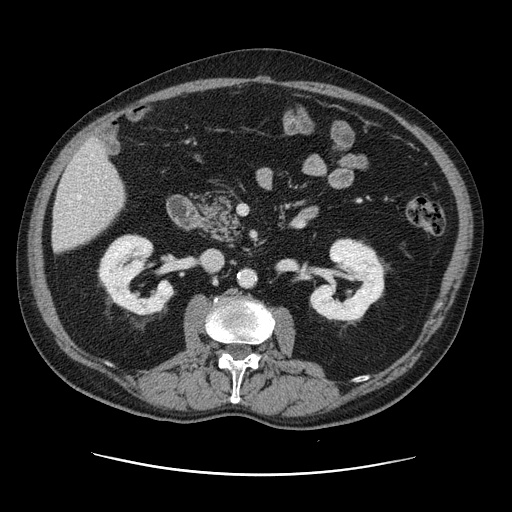
Contrast-enhanced abdominal CT, one axial slice; slice 46 of 141 in the series (ordered by position); 120 kVp; intravenous contrast given; soft-tissue window (W 400 / L 40 HU); 512 × 512 image matrix, field of view 395 × 395 mm. Male patient, age 72 years. Case-level facts recorded for this patient, not image findings: diagnosis: colorectal cancer liver metastases, imaged before liver resection; multiple liver metastases: yes; largest metastasis: 5.4 cm; chemotherapy before resection: yes.
Structures marked on this image (manually delineated by an expert):
- hepatic veins: bounding box (x1, y1, x2, y2) in pixels: (69, 195, 93, 203)
- liver: (54, 140, 126, 252)
- planned liver remnant (the part of the liver to remain after resection): (53, 159, 126, 252)